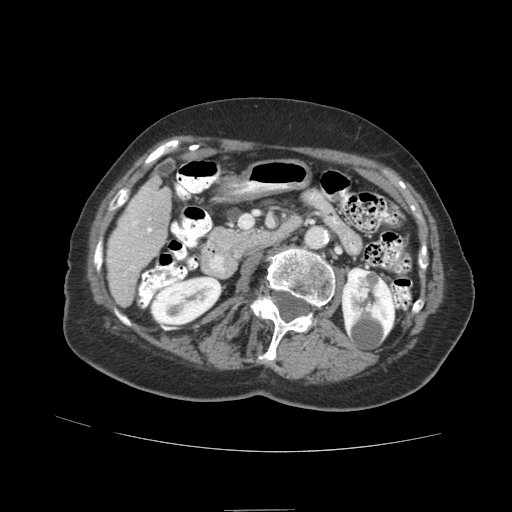
Contrast-enhanced abdominal CT (liver protocol), one axial slice; position 27 of 89 along the scan axis; reconstruction kernel STANDARD; 140 kVp; soft-tissue window (W 400 / L 40 HU); 2.5 mm slice thickness; 512 × 512 image matrix, field of view 360 × 360 mm. From the clinical record (not read from this slice): diagnosis: hepatocellular carcinoma (patient treated with transarterial chemoembolisation; whether this scan precedes or follows treatment is not stated here); TNM stage (as recorded): Stage-II; Child-Pugh class: A; tumour differentiation: moderately differentiated; tumour nodularity: multinodular.
Structures marked on this image (semi-automatic segmentation, software-assisted and operator-edited):
- liver parenchyma outside the tumour (the mass and vessels are separate outlines, so this box may not span the whole liver): bounding box <106,177,170,306> (left, top, right, bottom; pixels)
- liver vessels: <129,221,152,269>